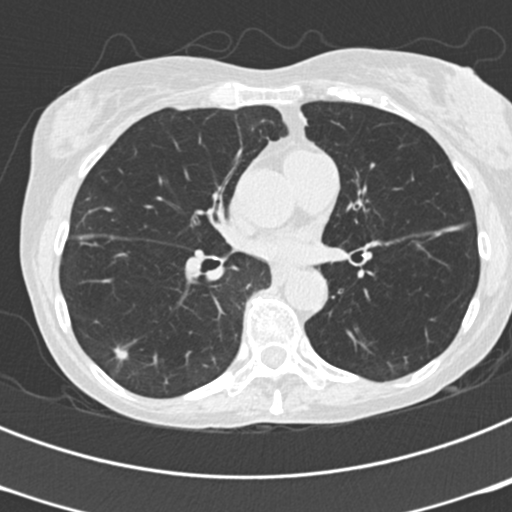
Axial slice from a low-dose chest CT screening exam. Third screening round (two years after baseline). Lung window (W 1500 / L -600 HU). 2 mm slice thickness. Standard (soft-tissue) reconstruction kernel (B30f). 120 kVp. Slice 92 of 199 in the series. Female participant, aged 68 years at enrolment.
Expert-annotated lung lesion, bounding box (x1, y1, x2, y2) in pixels: (102, 336, 140, 367). Reader record for this screening exam (exam-level; its link to the box is not recorded): non-calcified nodule or mass ≥4 mm, right lower lobe, 9 × 5 mm, poorly defined margins, soft tissue attenuation, pre-existing on the prior screen: yes; interval growth: no. Official screen result: positive, no significant change: stable abnormalities potentially related to lung cancer, unchanged since the prior screening exam. Lung cancer was diagnosed 310 days after this screen: squamous cell carcinoma, NOS, right lower lobe, stage IA (AJCC 6th edition).